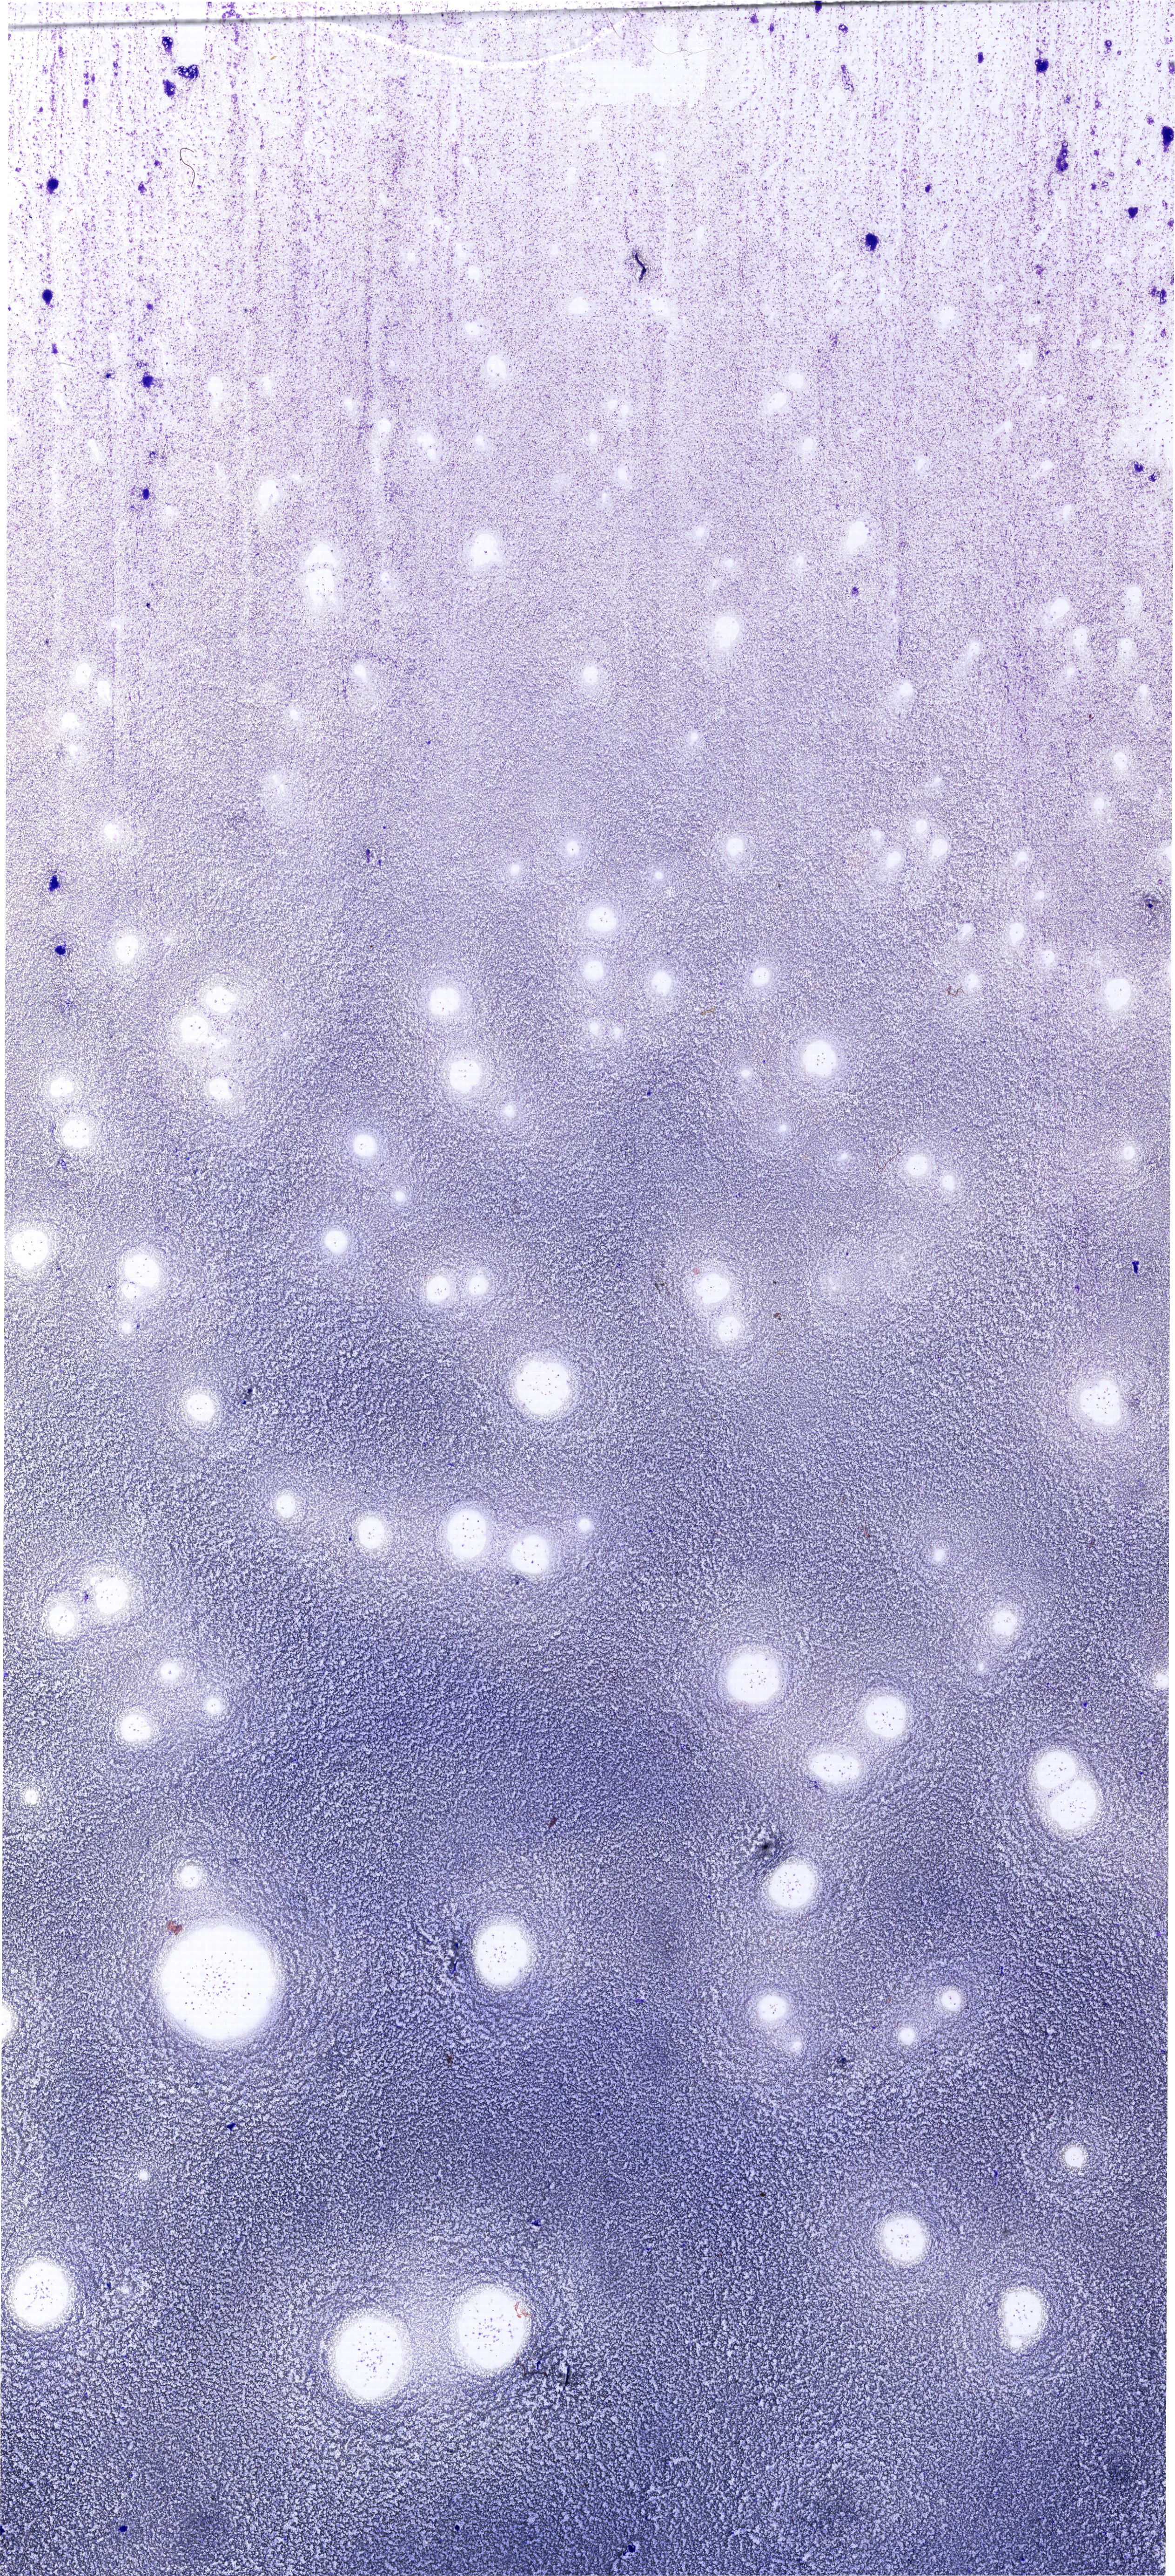
Whole-slide image of a May-Grünwald-Giemsa (MGG)-stained bone marrow aspirate smear — a low-resolution overview of the entire scanned area, about 19.7 x 43.2 mm. Patient sex: male.
Diagnosis: Mixed Phenotype Acute Leukemia, B/Myeloid.